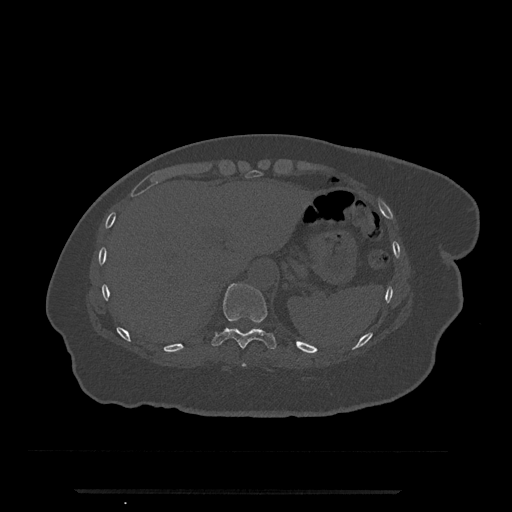
CT including the spine, one axial slice; position 284 of 797 along the scan axis; reconstruction kernel Br40s/3; bone window (W 1800 / L 400 HU); 0.5 mm slice thickness; 512 × 512 image matrix, field of view 440 × 440 mm. Female patient, age 51 years. From the clinical record (not read from this slice): primary cancer: neuro.
Outlined on this slice (semi-automatically segmented with operator editing):
- T10 vertebra: bounding box <212,283,277,350> (left, top, right, bottom; pixels)
- T9 vertebra: <242,363,246,367>